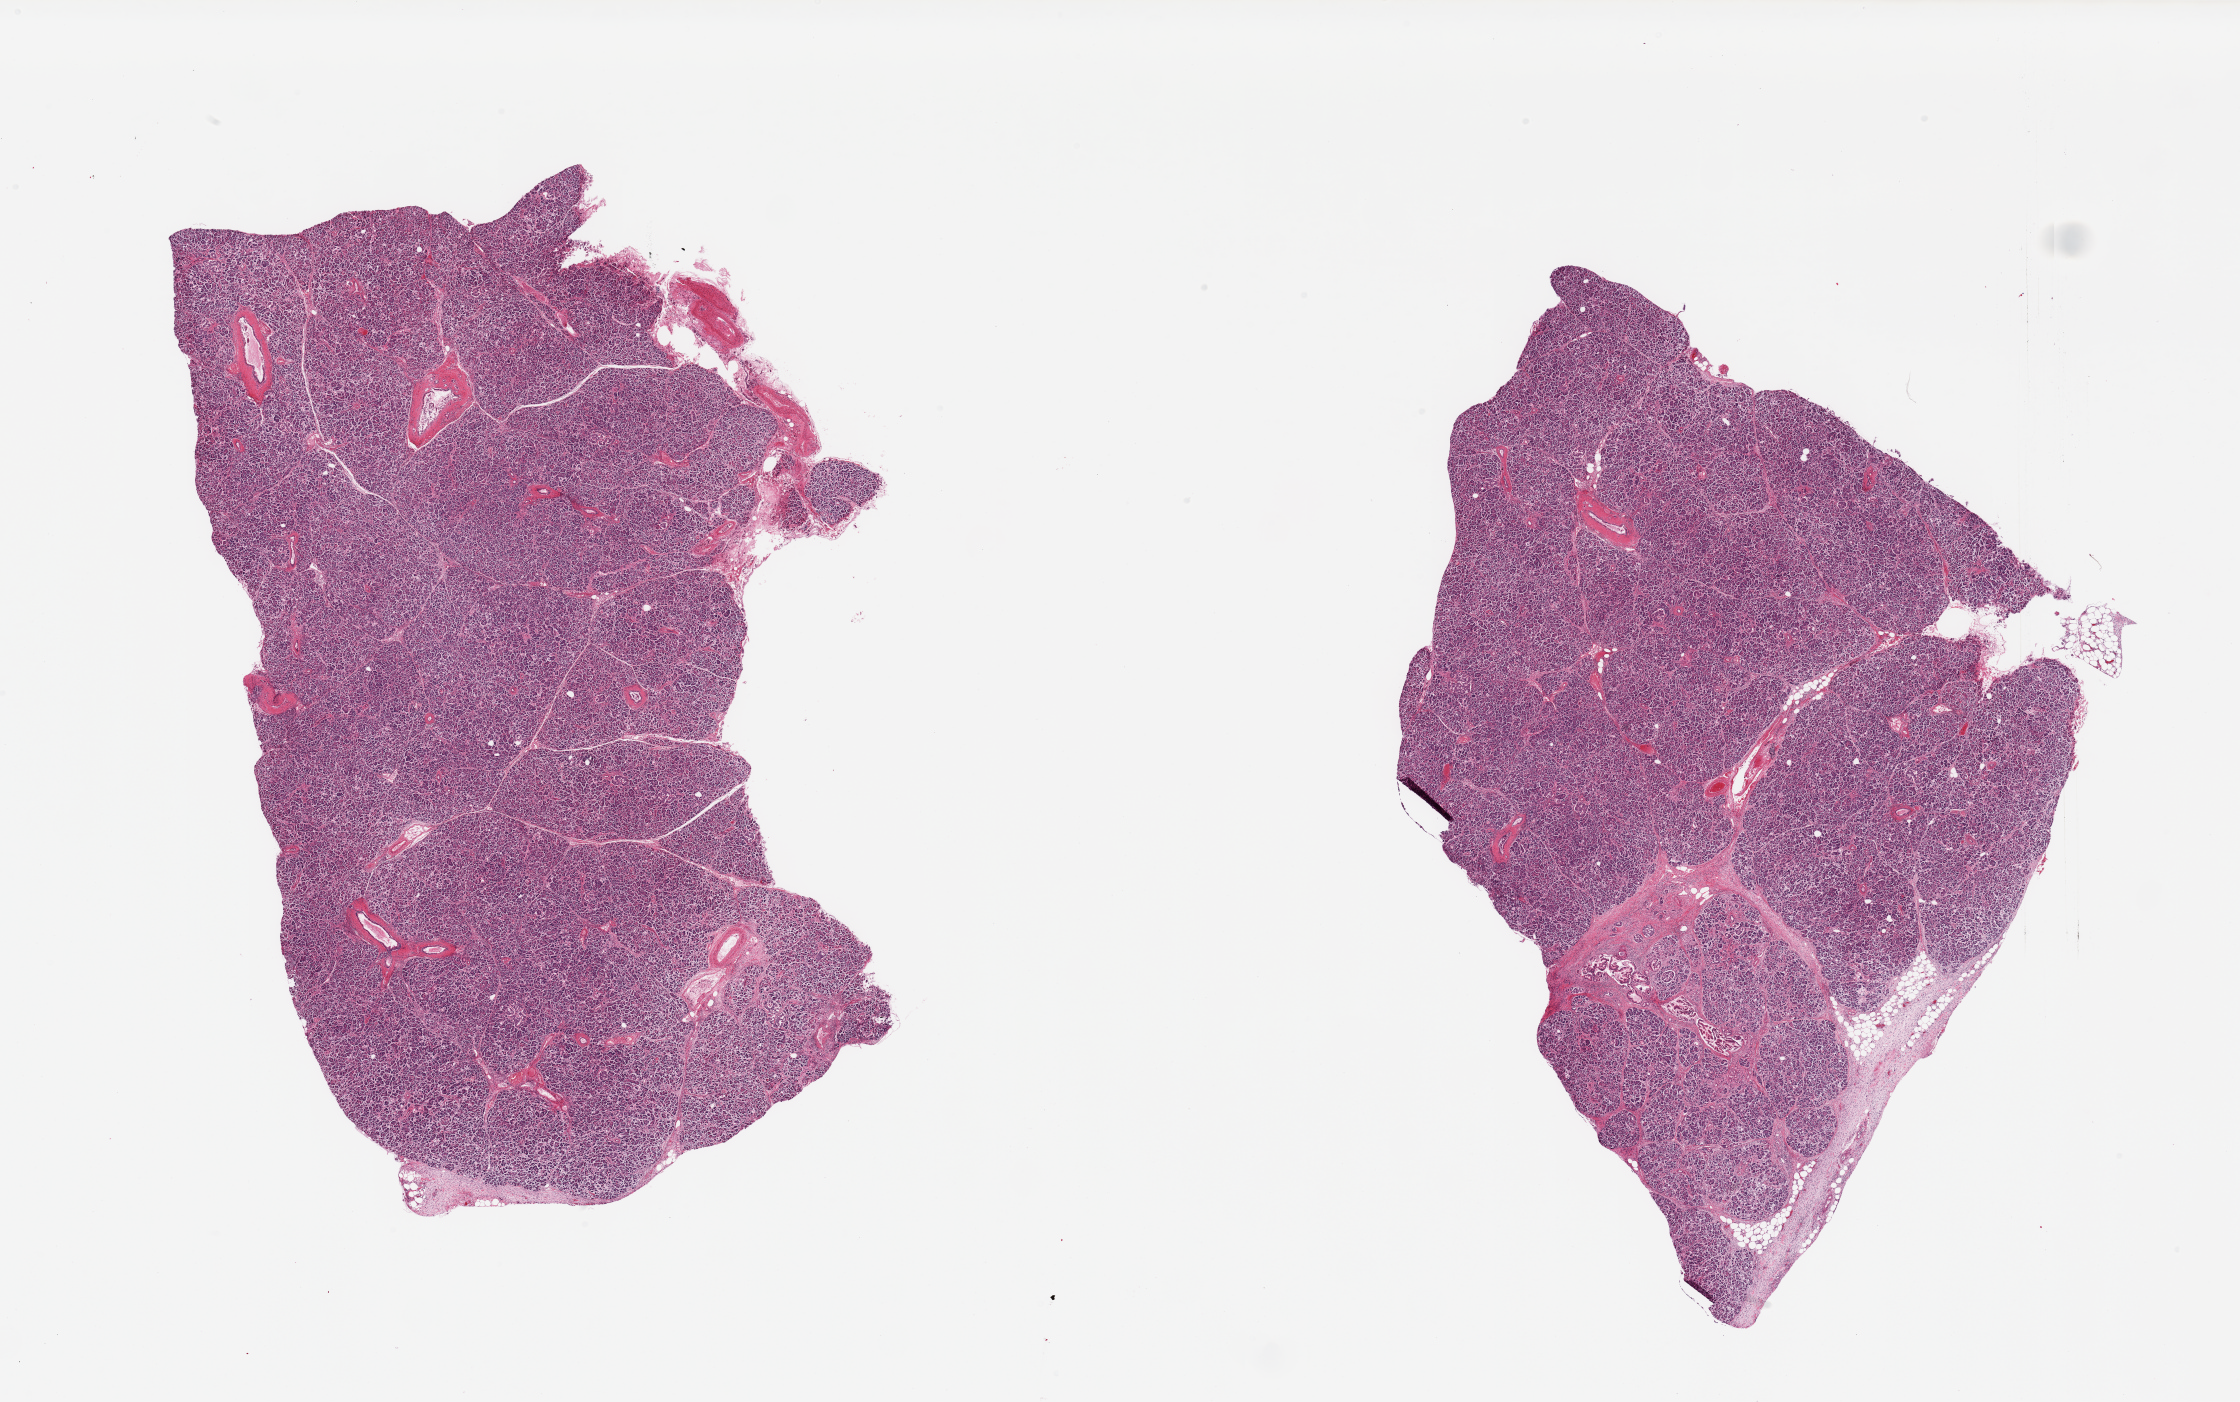
Whole-slide image, H&E stain, brightfield — low-resolution overview of the scanned area, about 35.4 x 22.2 mm. PAXgene-fixed paraffin-embedded (PFPE) section. Target tissue: pancreas. Tissue donor sample. Male donor.
• pathologist's review note for this sample: 2 pieces; minimal fat content